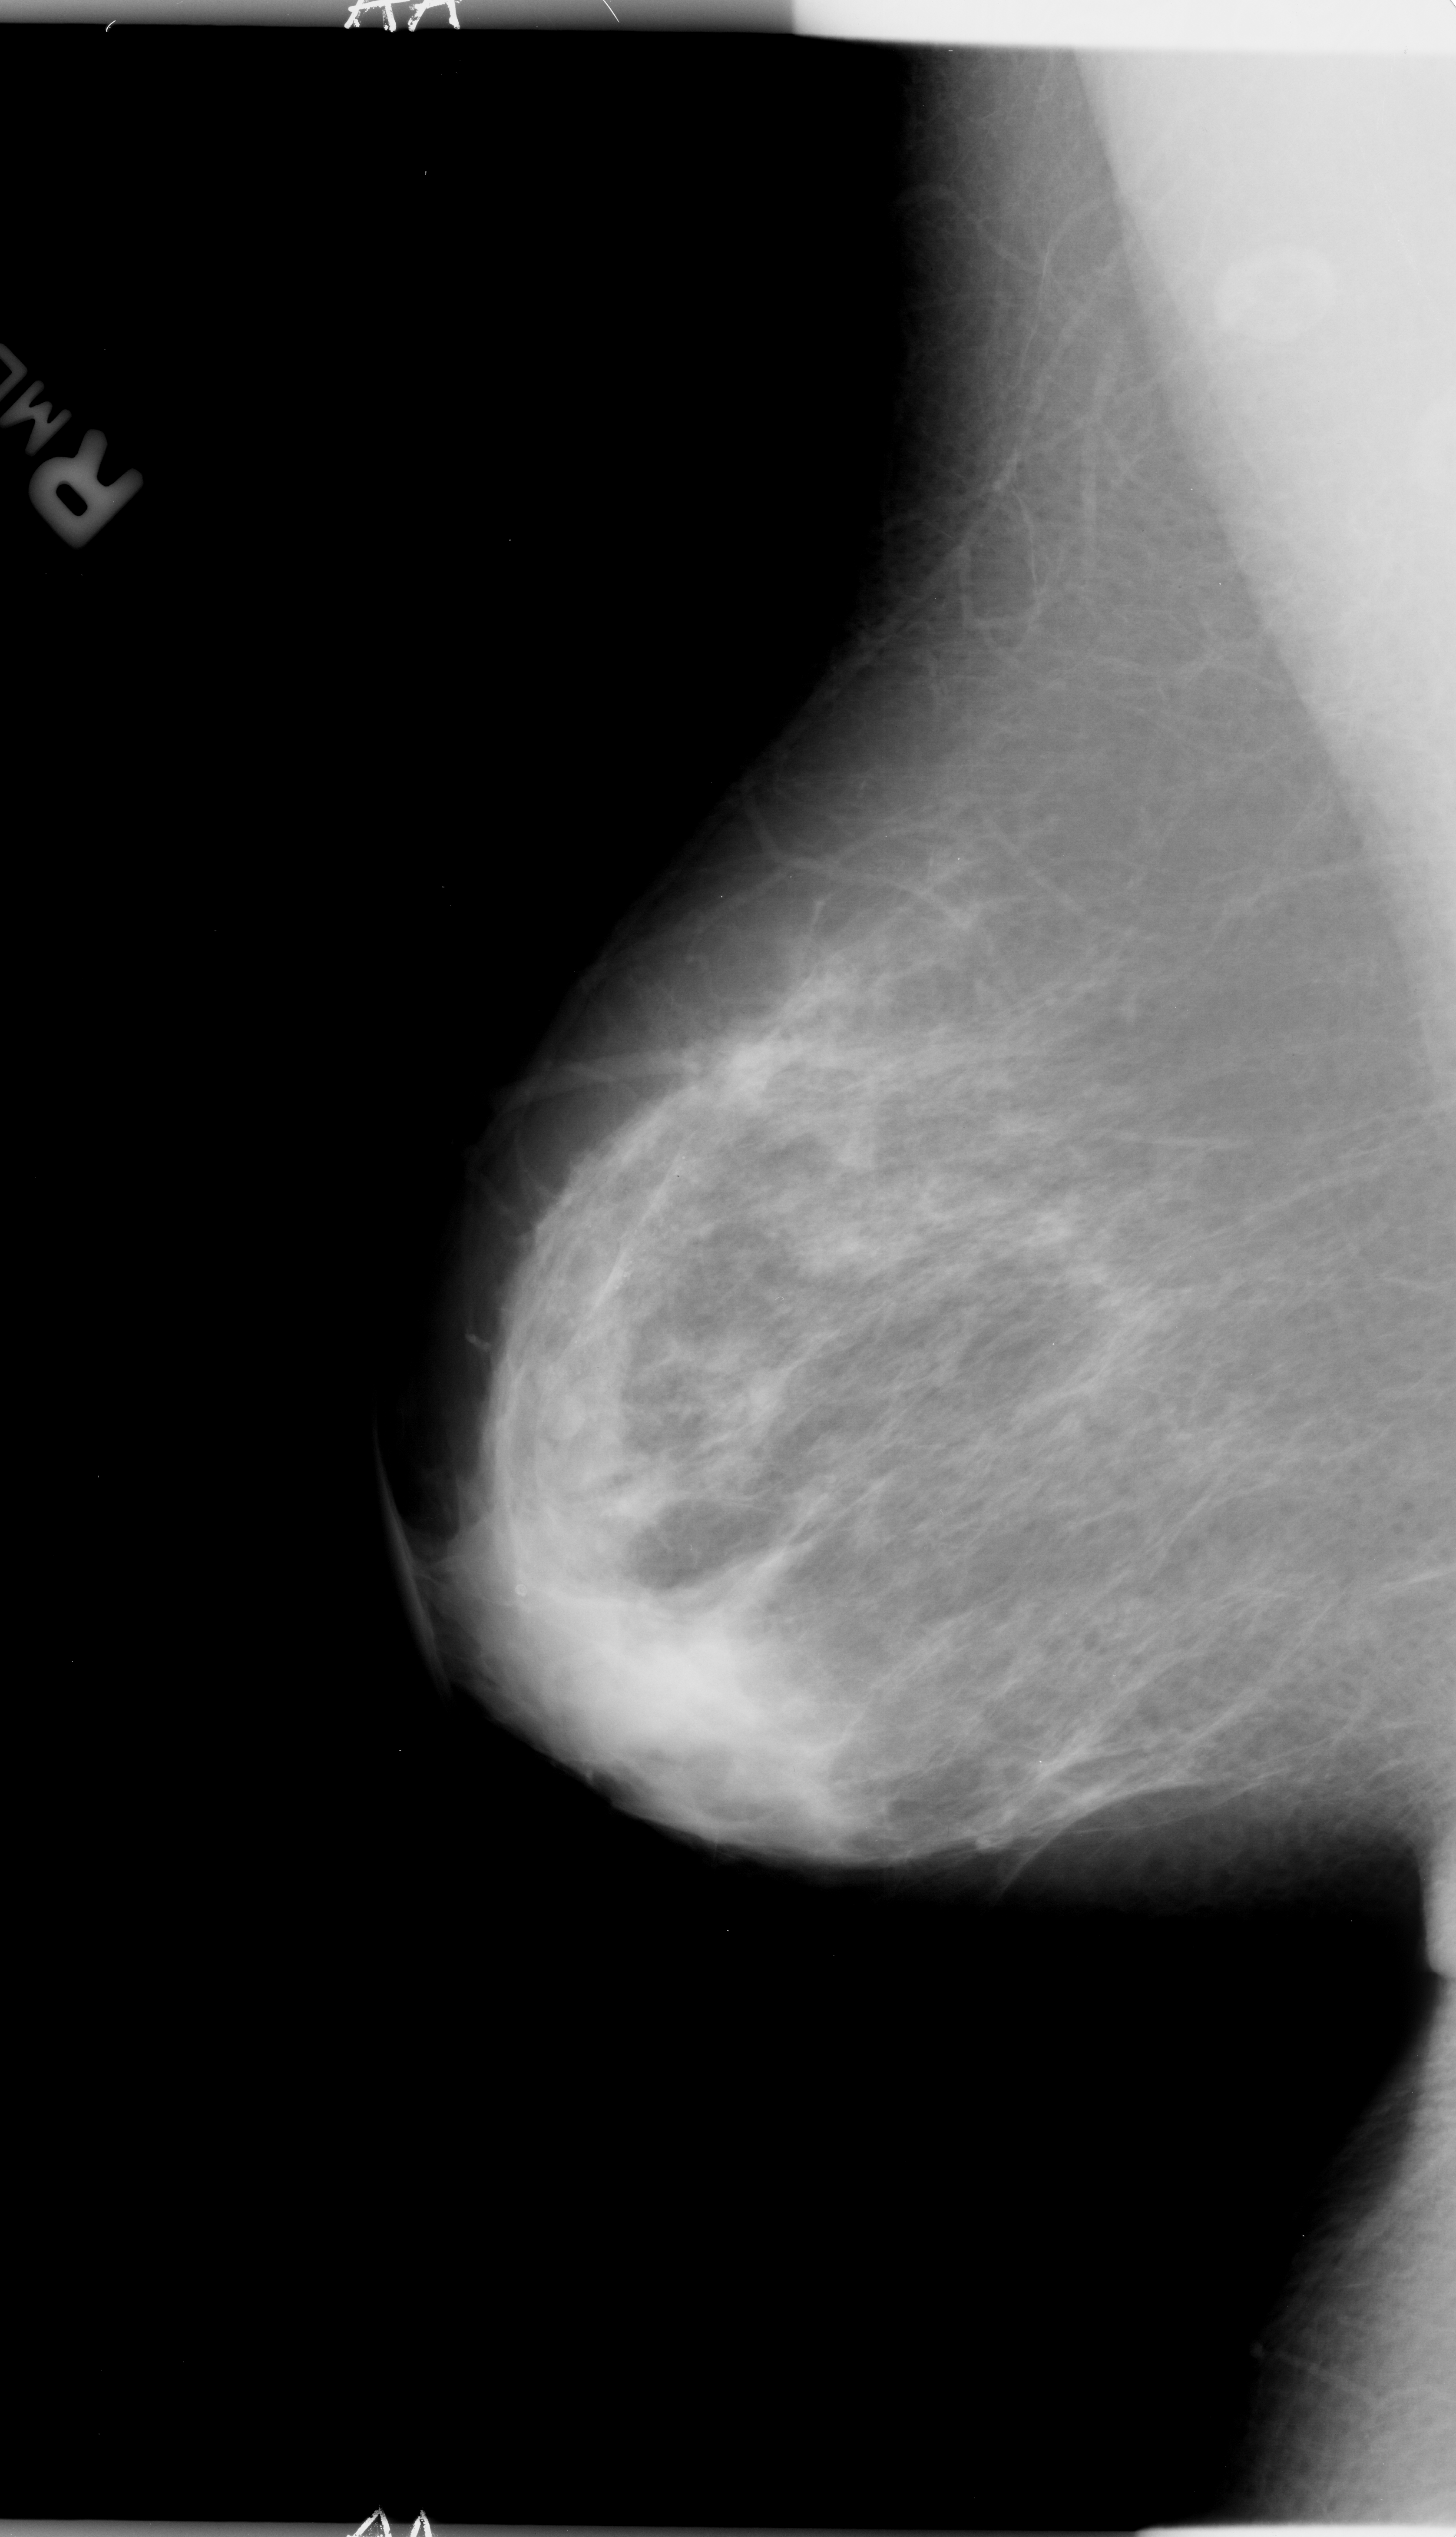
Digitized screen-film mammogram; right breast; MLO view; breast composition: heterogeneously dense (BI-RADS density category 3 of 4); 1456 × 2537 image matrix.
Expert-marked regions of interest on this film, with their recorded descriptors:
- calcifications, morphology pleomorphic, distribution segmental; BI-RADS assessment category 4; pathology result (as recorded, not read from the image): benign: bounding box <552,1126,758,1363> (left, top, right, bottom; pixels)